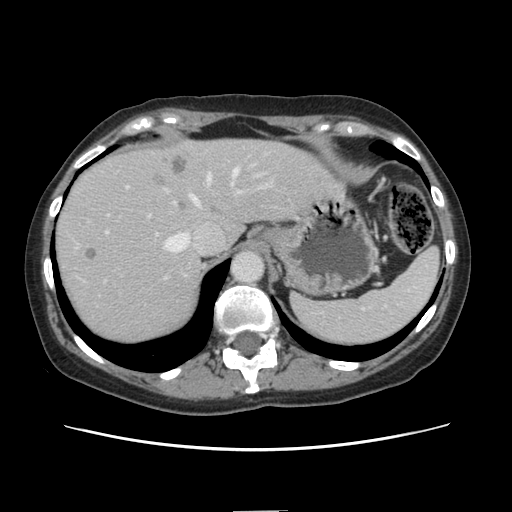
Contrast-enhanced abdominal CT, one axial slice; slice 111 of 141 in the series (ordered by position); 120 kVp; soft-tissue window (W 400 / L 40 HU); 2.5 mm slice thickness; 512 × 512 image matrix, field of view 350 × 350 mm. Female patient, age 63 years. From the clinical record (not read from this slice): diagnosis: colorectal cancer liver metastases, imaged before liver resection; multiple liver metastases: yes; largest metastasis: 3.2 cm; disease in both lobes: yes.
Outlined on this slice (expert manual segmentation):
- hepatic veins: bounding box <165,169,239,252> (left, top, right, bottom; pixels)
- liver: <55,139,337,345>
- planned liver remnant (the part of the liver to remain after resection): <193,140,339,242>
- portal vein (with intrahepatic branches): <198,176,241,205>
- liver metastasis: <152,173,166,187>